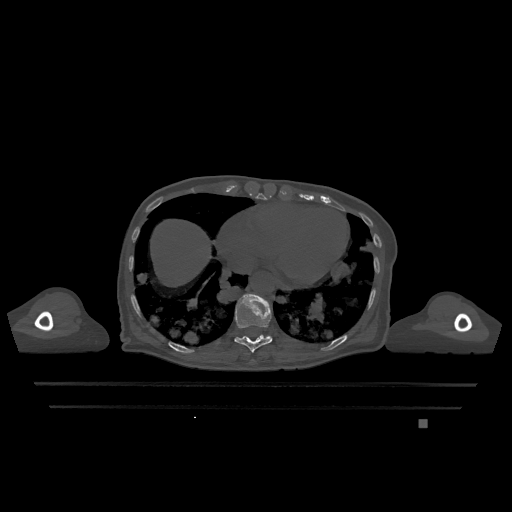
CT including the spine, one axial slice; position 634 of 1317 along the scan axis; bone window (W 1800 / L 400 HU); 0.5 mm slice thickness; 512 × 512 image matrix, field of view 500 × 500 mm. Patient: female, 74 years. Case-level facts recorded for this patient, not image findings: primary cancer: lung; vertebrae with lytic lesions (as recorded): T1, T4, T5, T6, L4, L5.
Outlined on this slice (semi-automatically segmented with operator editing):
- T10 vertebra: box from (x=234, y=294) to (x=272, y=353) px